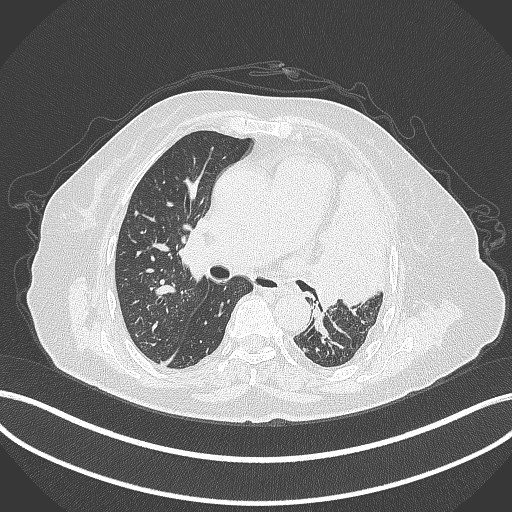
Chest CT, one axial slice; position 218 of 399 along the scan axis; 120 kVp; lung window (W 1500 / L -600 HU); 1 mm slice thickness; 512 × 512 image matrix, field of view 400 × 400 mm. Patient: female, 75 years. Case-level facts recorded for this patient, not image findings: clinical TNM (as recorded): T3 N3 M1.
Outlined on this slice (bounding box drawn by a radiologist):
- lung tumour (recorded histology: adenocarcinoma): bounding box (x1, y1, x2, y2) in pixels: (307, 166, 398, 314)